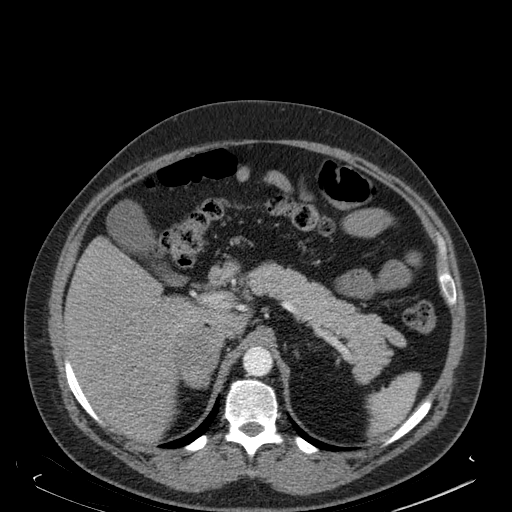
Contrast-enhanced abdominal CT, one axial slice; slice 123 of 181 in the series (ordered by position); soft-tissue window (W 400 / L 40 HU); 1.5 mm slice thickness; 512 × 512 image matrix, field of view 405 × 405 mm. Male patient. From the clinical record (not read from this slice): diagnosis: adrenocortical carcinoma; tumour side: right adrenal; tumour size at pathology: 7.5 cm; Ki-67 index: 25 %; stage (as recorded): 4.
Outlined on this slice (semi-automatically segmented with operator editing):
- mass: bounding box [x1, y1, x2, y2] px = [176, 332, 218, 387]